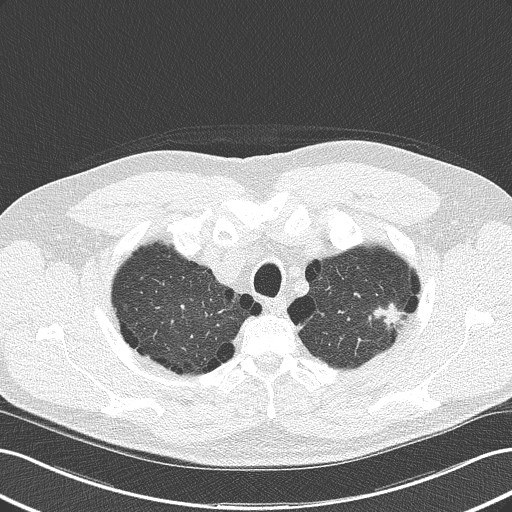
Chest CT (low-dose screening protocol), one axial image, second annual screen, lung window (W 1500 / L -600 HU), 2 mm slice thickness. Male, age 62 years at enrolment.
• Expert-annotated lung lesion, box from (x=356, y=288) to (x=415, y=339) px.
• The screening reader recorded 2 non-calcified nodules or masses ≥4 mm on this exam; which of them this box marks is not recorded.
• Official screen result: positive, other.
• Participant outcome: lung cancer diagnosed 46 days after this screen — adenocarcinoma, NOS, left upper lobe, well differentiated (G1), stage IB (AJCC 6th edition), 17 mm at pathology.